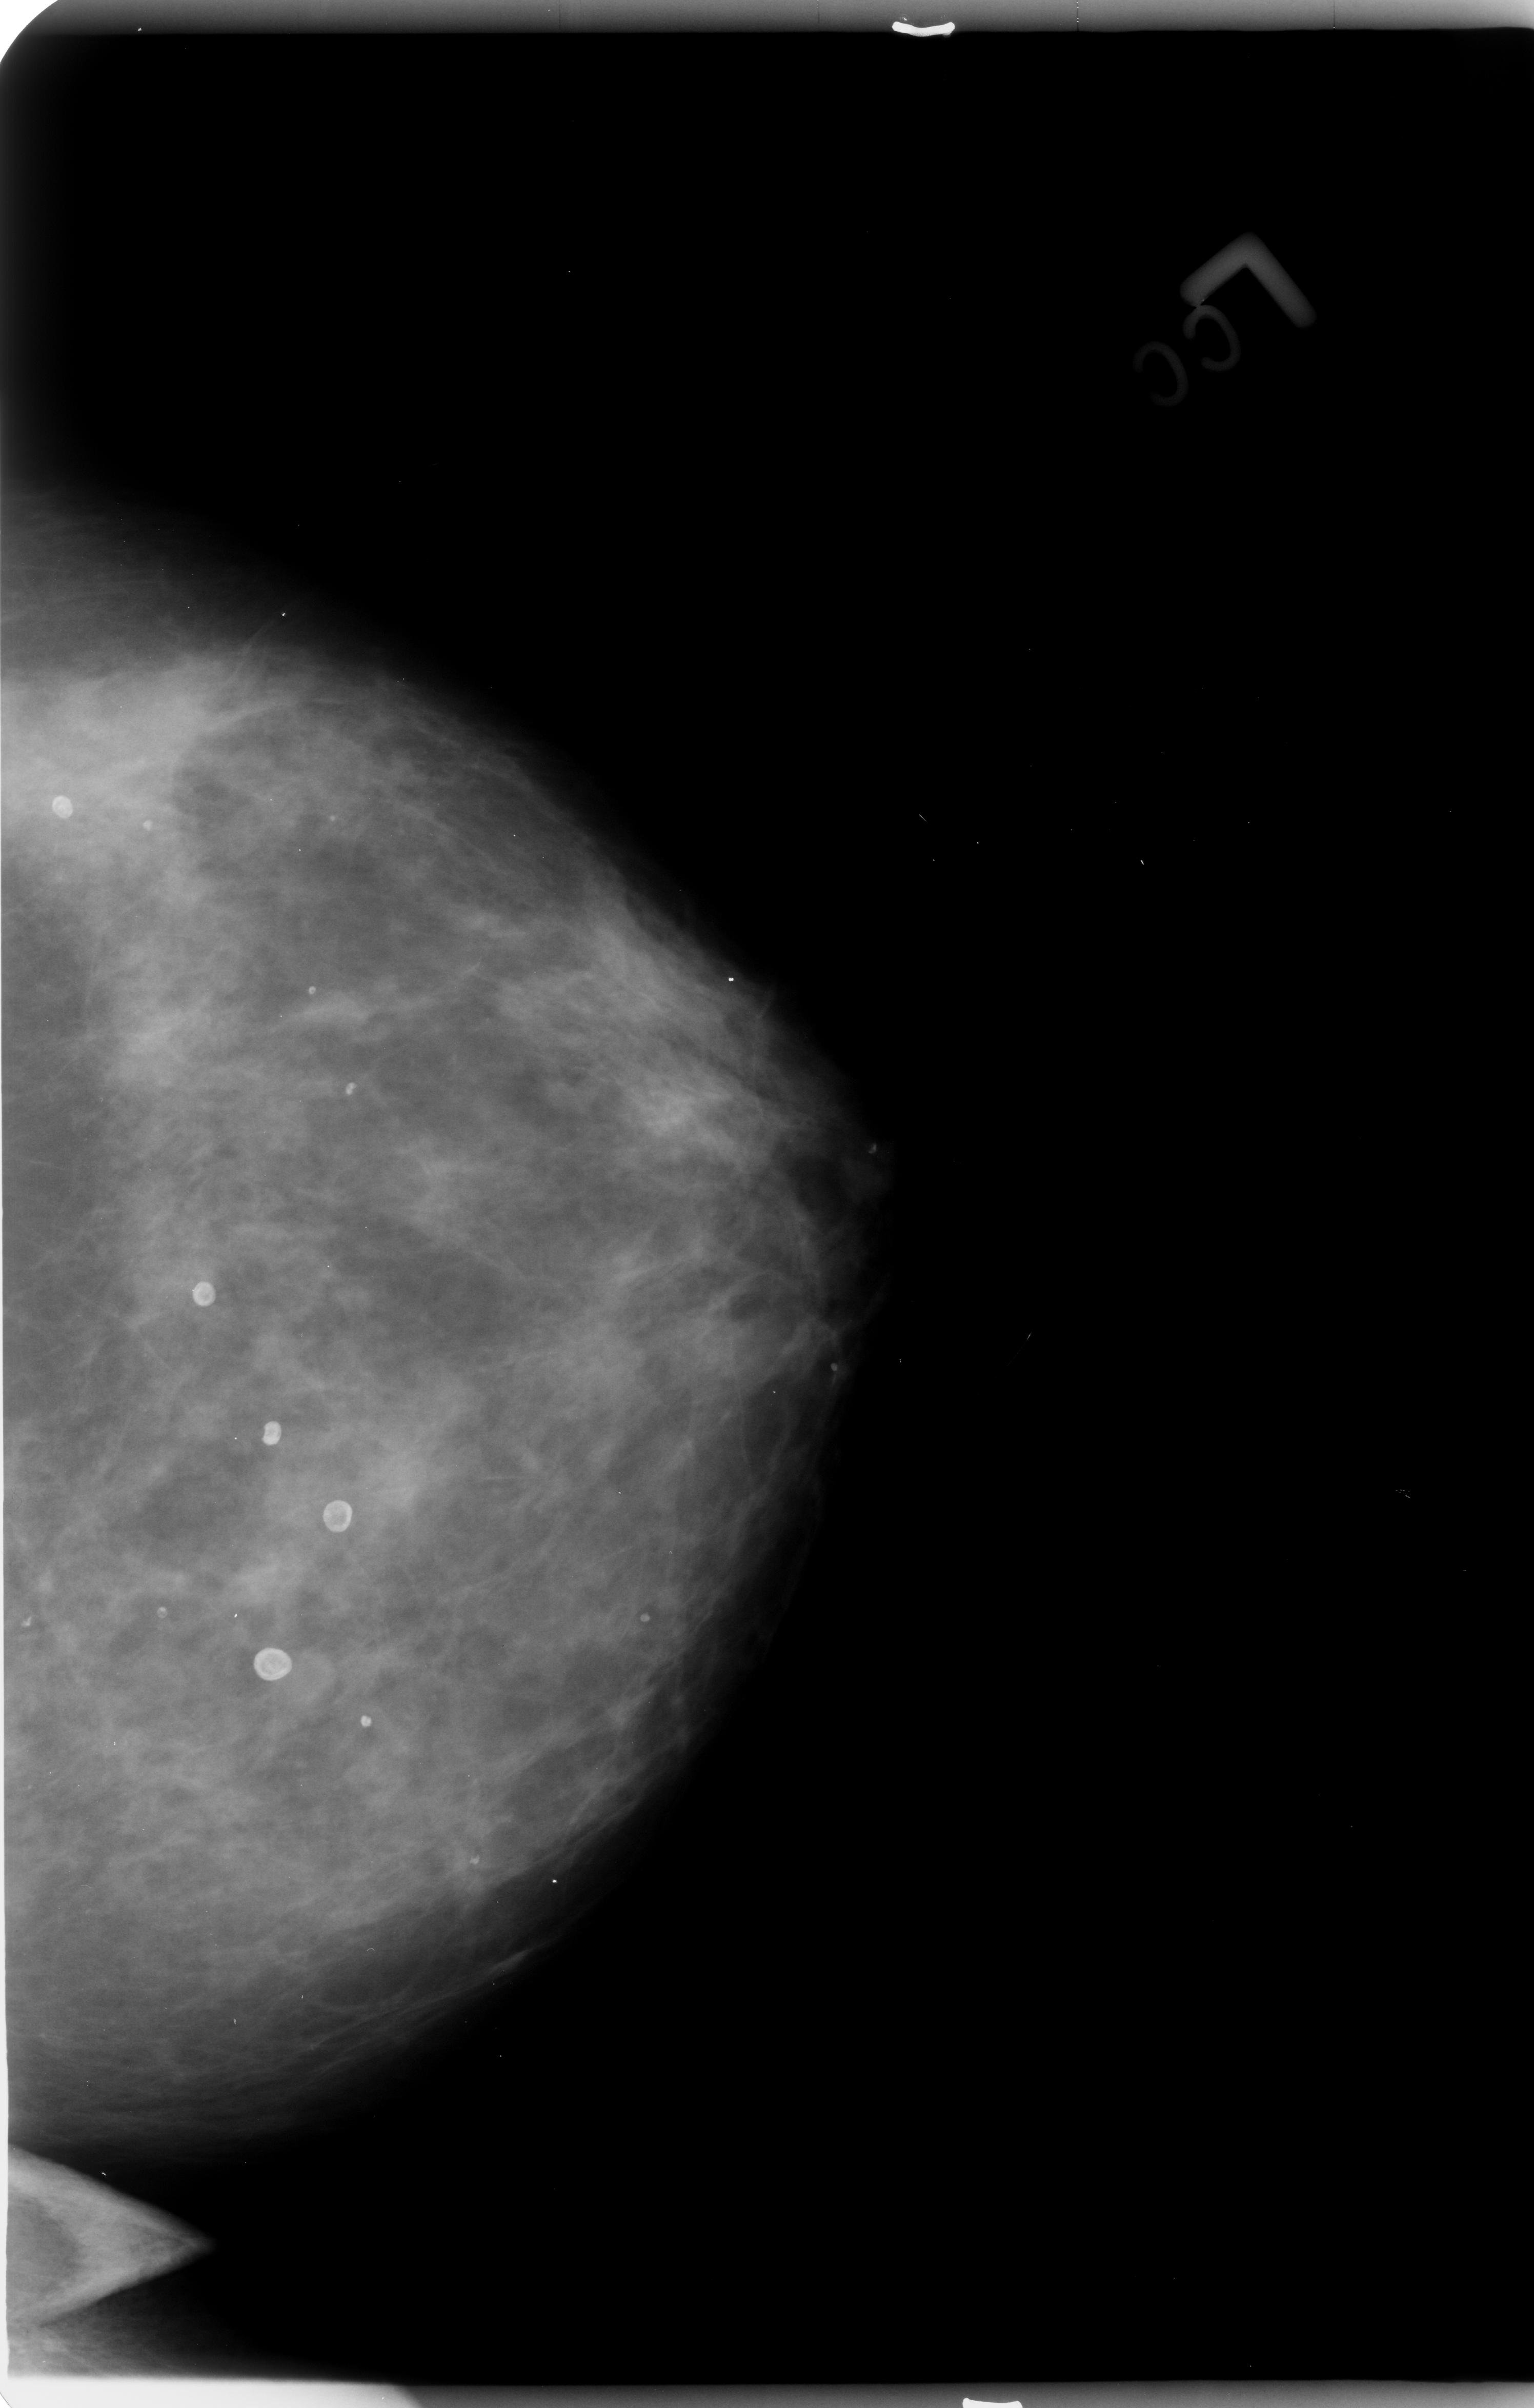
Mammogram (digitized film). Left breast. Craniocaudal (CC) view. BI-RADS breast density category 3 (scale 1–4). 1534 × 2408 image matrix.
Marked abnormalities (boxes around the expert regions of interest):
- Finding 1 of 4: calcifications, morphology round and regular / eggshell; BI-RADS assessment category 2; benign; no additional work-up was recommended (outcome (as recorded, no biopsy): benign without callback): bounding box <164,1251,231,1326> (left, top, right, bottom; pixels)
- Finding 2 of 4: calcifications, morphology round and regular / eggshell; BI-RADS assessment category 2; benign; no additional work-up was recommended (outcome (as recorded, no biopsy): benign without callback): <217,1620,321,1712>
- Finding 3 of 4: calcifications, morphology round and regular / eggshell; BI-RADS assessment category 2; benign; no additional work-up was recommended (outcome (as recorded, no biopsy): benign without callback): <246,1394,309,1461>
- Finding 4 of 4: calcifications, morphology round and regular / eggshell; BI-RADS assessment category 2; benign; no additional work-up was recommended (outcome (as recorded, no biopsy): benign without callback): <299,1476,370,1560>